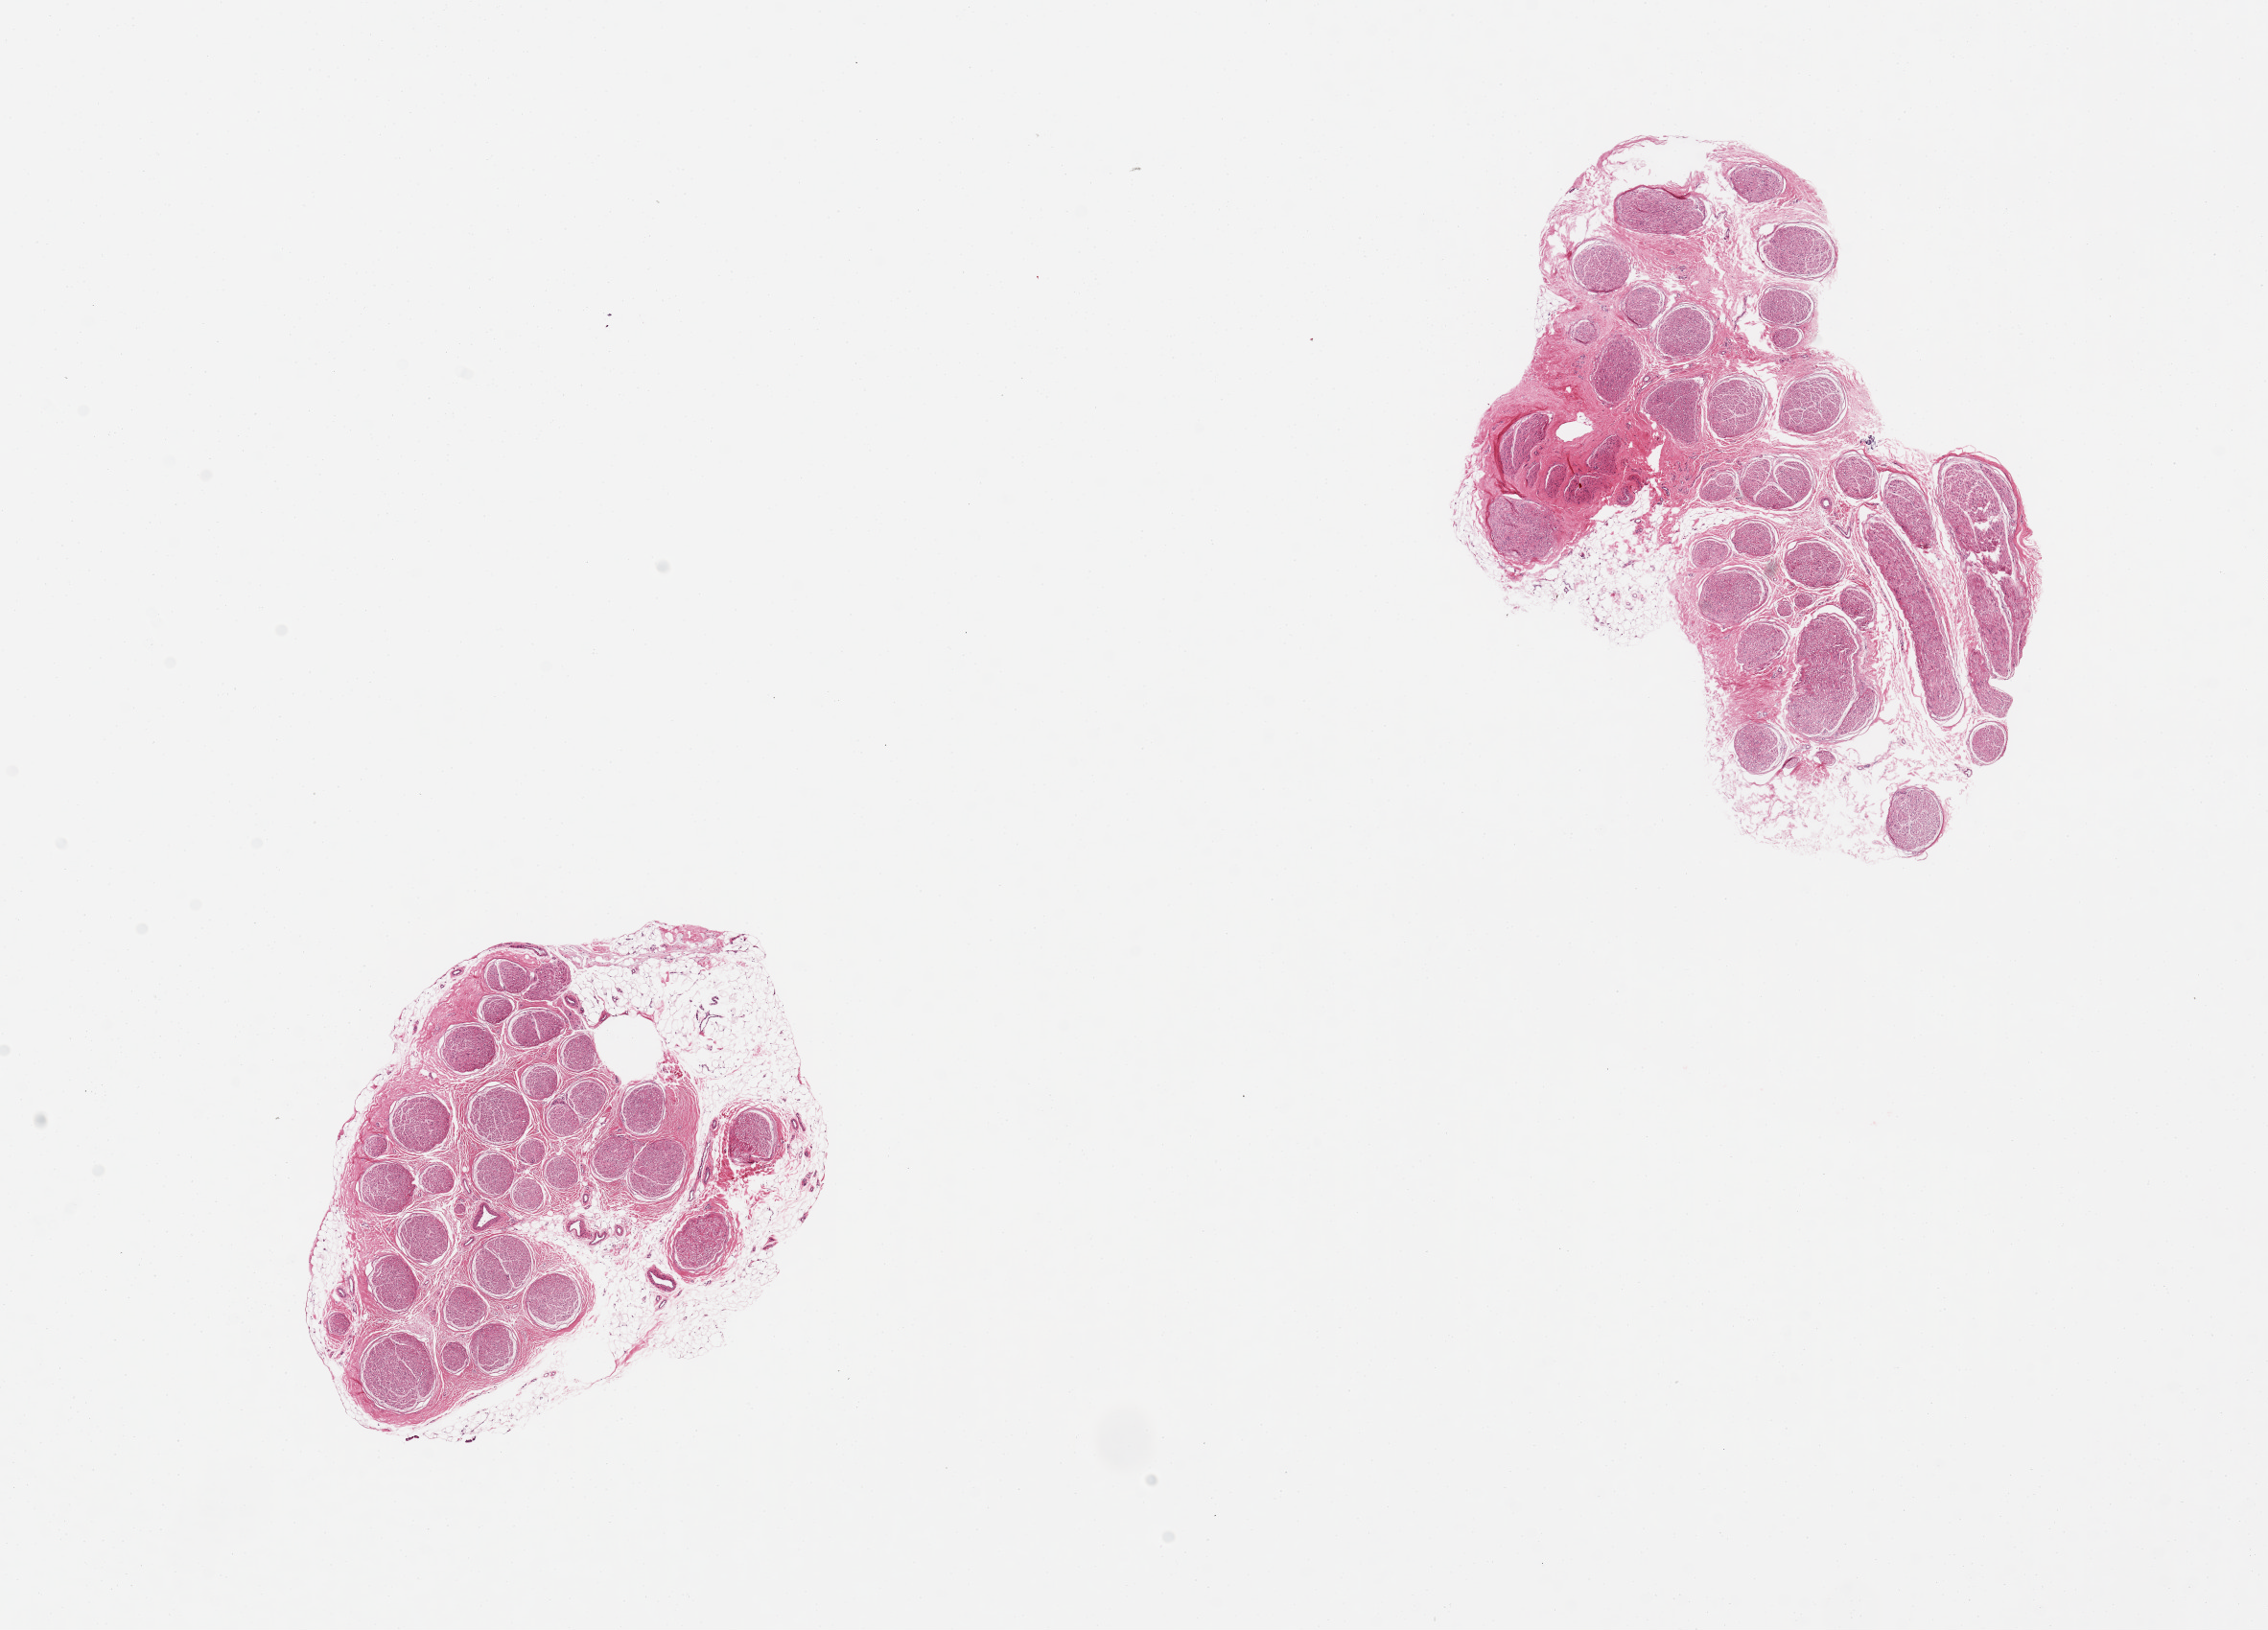
Digitized haematoxylin and eosin-stained section — low-resolution overview of the scanned area, about 18.7 x 13.4 mm (from a 20x scan), PAXgene-fixed paraffin-embedded (PFPE) section, target tissue: tibial nerve, tissue donor sample. Female donor.
Review note (as recorded): 2 pieces, 5x4 & 6x4mm; 25% adherent adipose.